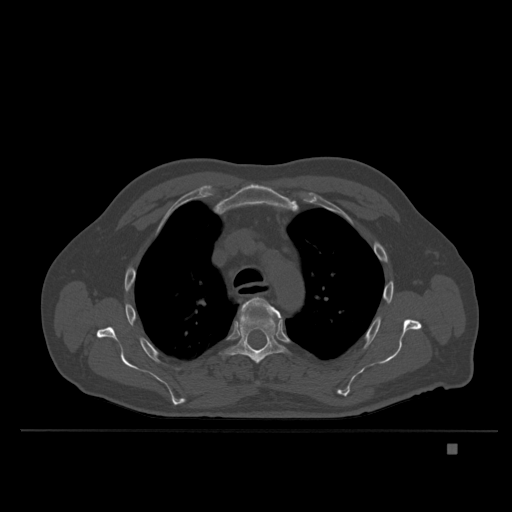
CT including the spine, one axial slice; position 277 of 435 along the scan axis; bone window (W 1800 / L 400 HU); 1.5 mm slice thickness; 512 × 512 image matrix. Male patient, age 73 years. Case-level facts recorded for this patient, not image findings: primary cancer: skin.
Outlined on this slice (semi-automatically segmented with operator editing):
- T4 vertebra: bounding box (x1, y1, x2, y2) in pixels: (239, 297, 281, 384)
- T5 vertebra: (221, 308, 292, 364)